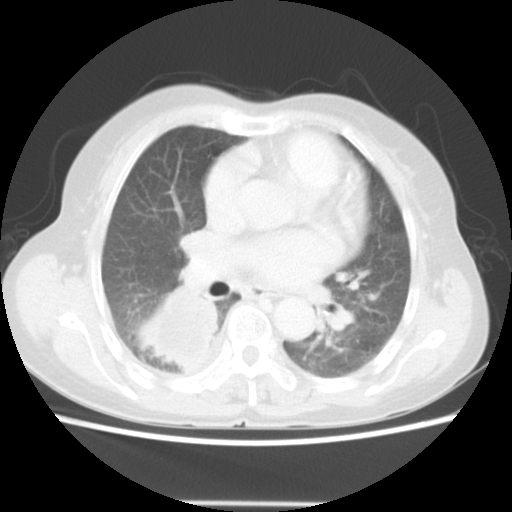
Chest CT, one axial slice. Position 27 of 52 along the scan axis. Reconstruction kernel STANDARD. 140 kVp. Lung window (W 1500 / L -600 HU). 5 mm slice thickness. 512 × 512 image matrix, field of view 337 × 337 mm. Female patient, age 67 years. From the clinical record (not read from this slice): clinical TNM (as recorded): T3 N1 M1.
Structures marked on this image (rectangle marked by the reading radiologist):
- lung tumour (recorded histology: adenocarcinoma): bounding box (x1, y1, x2, y2) in pixels: (138, 282, 222, 377)